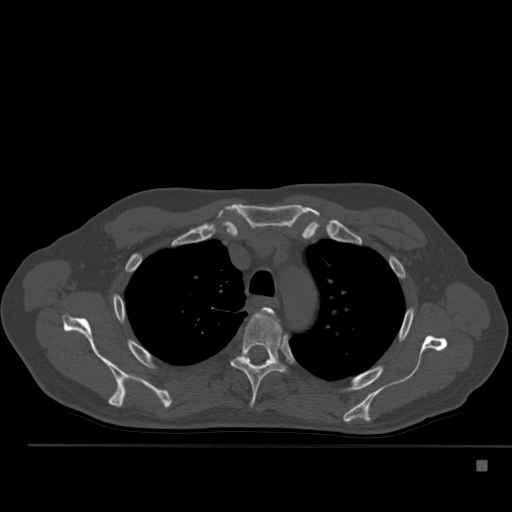
CT including the spine, one axial slice; slice 382 of 517 in the series (ordered by position); reconstruction kernel Br40s; 120 kVp; bone window (W 1800 / L 400 HU); 1.5 mm slice thickness; 512 × 512 image matrix, field of view 408 × 408 mm. Patient: male, 70 years. From the clinical record (not read from this slice): primary cancer: renal.
Structures marked on this image (semi-automatic segmentation, software-assisted and operator-edited):
- T3 vertebra: bounding box (x1, y1, x2, y2) in pixels: (262, 307, 273, 314)
- T4 vertebra: (231, 311, 284, 408)
- T5 vertebra: (268, 358, 270, 360)